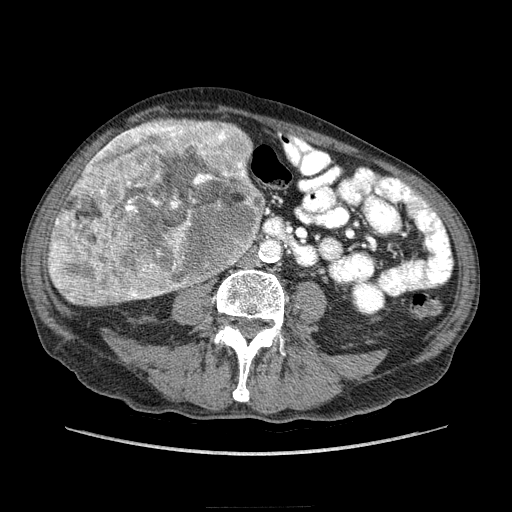
Contrast-enhanced abdominal CT (liver protocol), one axial slice. Position 57 of 218 along the scan axis. Reconstruction kernel STANDARD. Soft-tissue window (W 400 / L 40 HU). 2.5 mm slice thickness. 512 × 512 image matrix, field of view 380 × 380 mm. Case-level facts recorded for this patient, not image findings: diagnosis: hepatocellular carcinoma (patient treated with transarterial chemoembolisation; whether this scan precedes or follows treatment is not stated here); TNM stage (as recorded): Stage-IIIA; Child-Pugh class: A; tumour nodularity: multinodular; tumour size: 20 cm.
Outlined on this slice (semi-automatically segmented with operator editing):
- liver parenchyma outside the tumour (the mass and vessels are separate outlines, so this box may not span the whole liver): box from (x=48, y=124) to (x=251, y=303) px
- mass: (x=48, y=117)–(x=262, y=307)